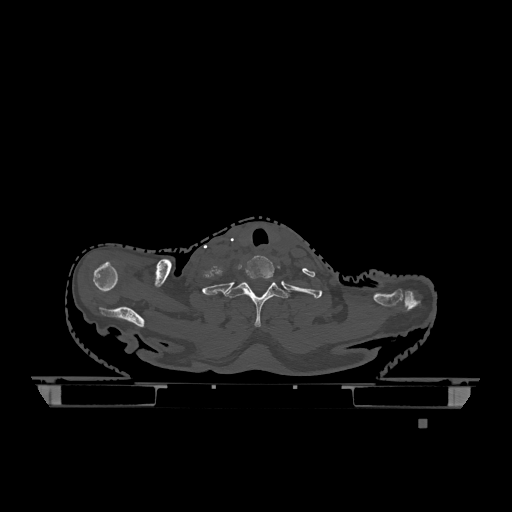
CT including the spine, one axial slice. Position 1007 of 1317 along the scan axis. Bone window (W 1800 / L 400 HU). 0.5 mm slice thickness. 512 × 512 image matrix, field of view 500 × 500 mm. Patient: female, 74 years. Case-level facts recorded for this patient, not image findings: primary cancer: lung; vertebrae with lytic lesions (as recorded): T1, T4, T5, T6, L4, L5.
Annotated regions visible in this slice (semi-automatically segmented with operator editing):
- T1 vertebra: bounding box <222,282,288,327> (left, top, right, bottom; pixels)